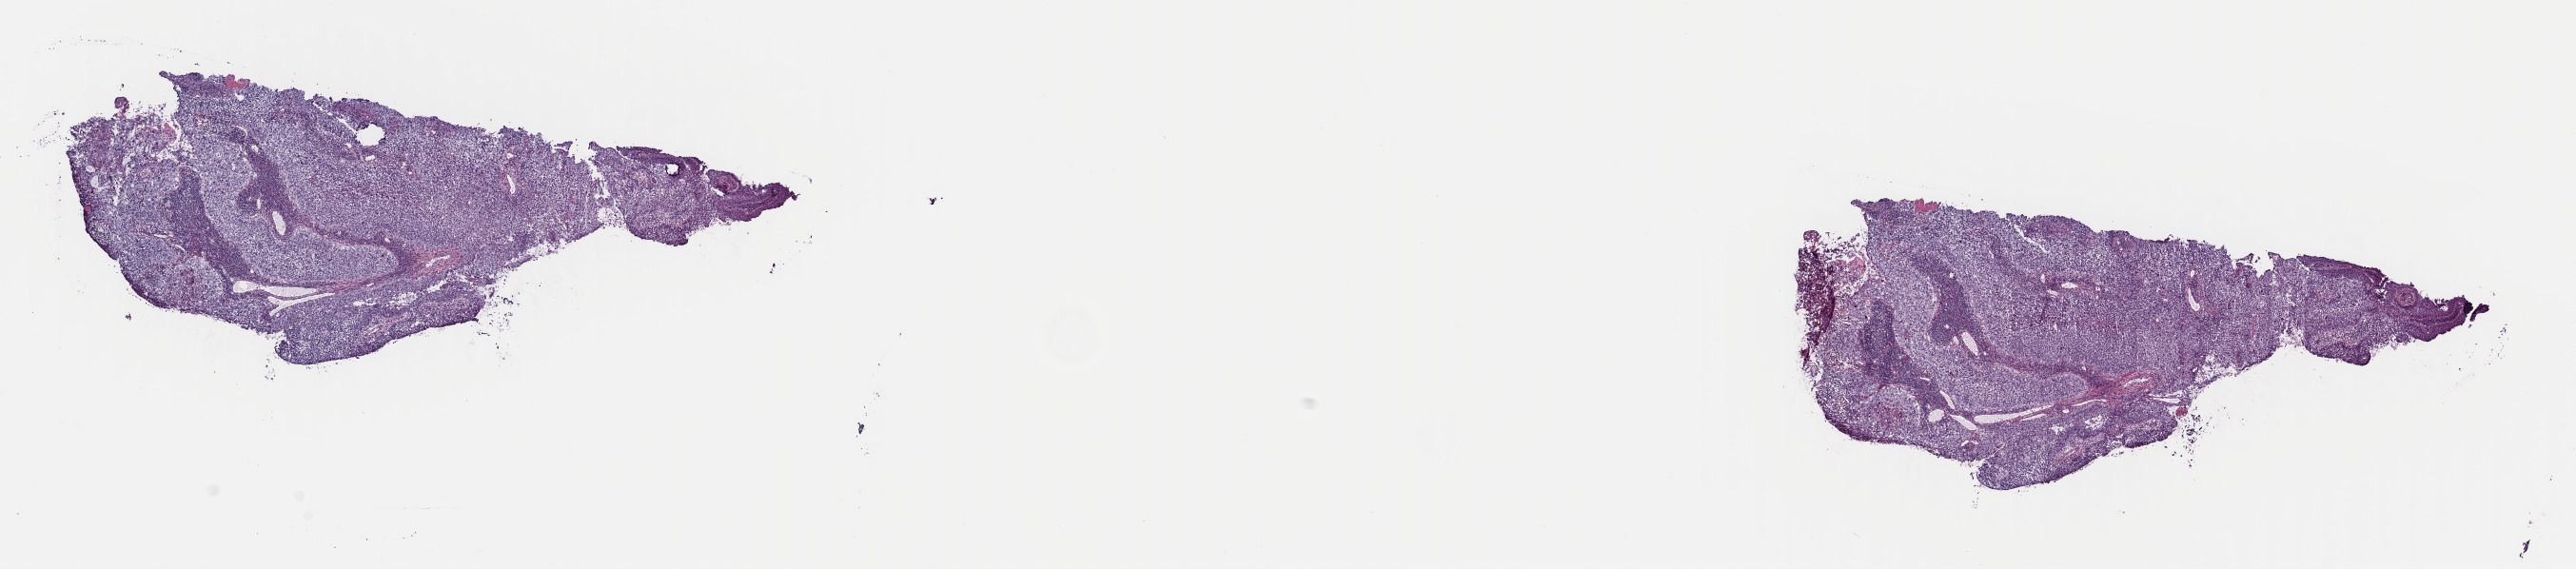
H&E whole-slide image, a low-resolution overview of the entire scanned area, about 21.4 x 4.7 mm, frozen section from the top of the tissue portion, sample: primary tumour, cervix. Female patient; age at initial diagnosis 41 years. Histologic grade: G3 (poorly differentiated). Composition of this section per pathologist review: tumour cells 100%, tumour nuclei 70%, normal cells 0%, stromal cells 0%, necrosis 0%. Inflammatory infiltration, as recorded: lymphocyte infiltration 10%, monocyte infiltration 0%, neutrophil infiltration 1%.
Histologic diagnosis: Squamous cell carcinoma, large cell, nonkeratinizing, NOS (cervix uteri). FIGO stage: IB1. Lymph nodes positive (case pathology): 0 of 26 examined.